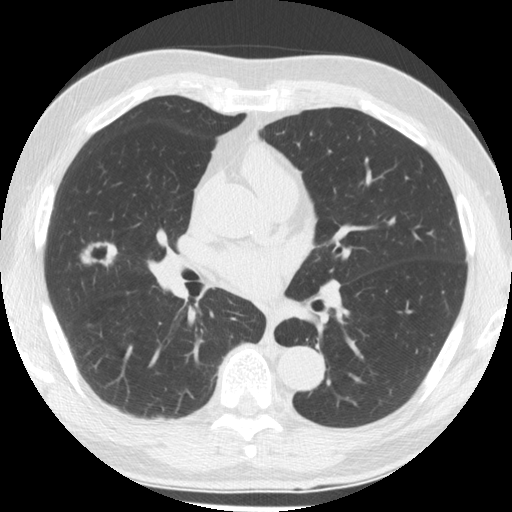
Low-dose screening chest CT, one axial slice; slice 99 of 176 in the series (ordered by position); 120 kVp; lung window (W 1500 / L -600 HU); 2.5 mm slice thickness; 512 × 512 image matrix, field of view 348 × 348 mm.
Outlined on this slice (manually delineated by an expert):
- lesion 1 (tumor, middle lobe of right lung): bounding box <81,242,118,267> (left, top, right, bottom; pixels)